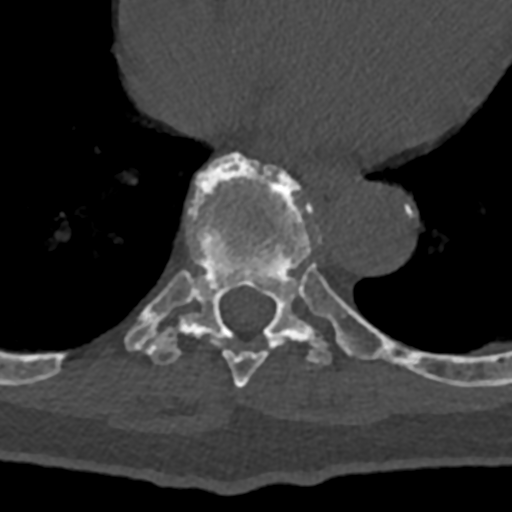
CT including the spine, one axial slice. Position 678 of 797 along the scan axis. Reconstruction kernel Br40s/3. Bone window (W 1800 / L 400 HU). 0.5 mm slice thickness. 512 × 512 image matrix, field of view 160 × 160 mm. Male patient, age 74 years. Case-level facts recorded for this patient, not image findings: primary cancer: renal; vertebrae with lytic lesions (as recorded): T10, L1, L2, L3, L4, L5.
Annotated regions visible in this slice (semi-automatically segmented with operator editing):
- T8 vertebra: box from (x=223, y=282) to (x=337, y=388) px
- T9 vertebra: (x=126, y=153)–(x=432, y=380)